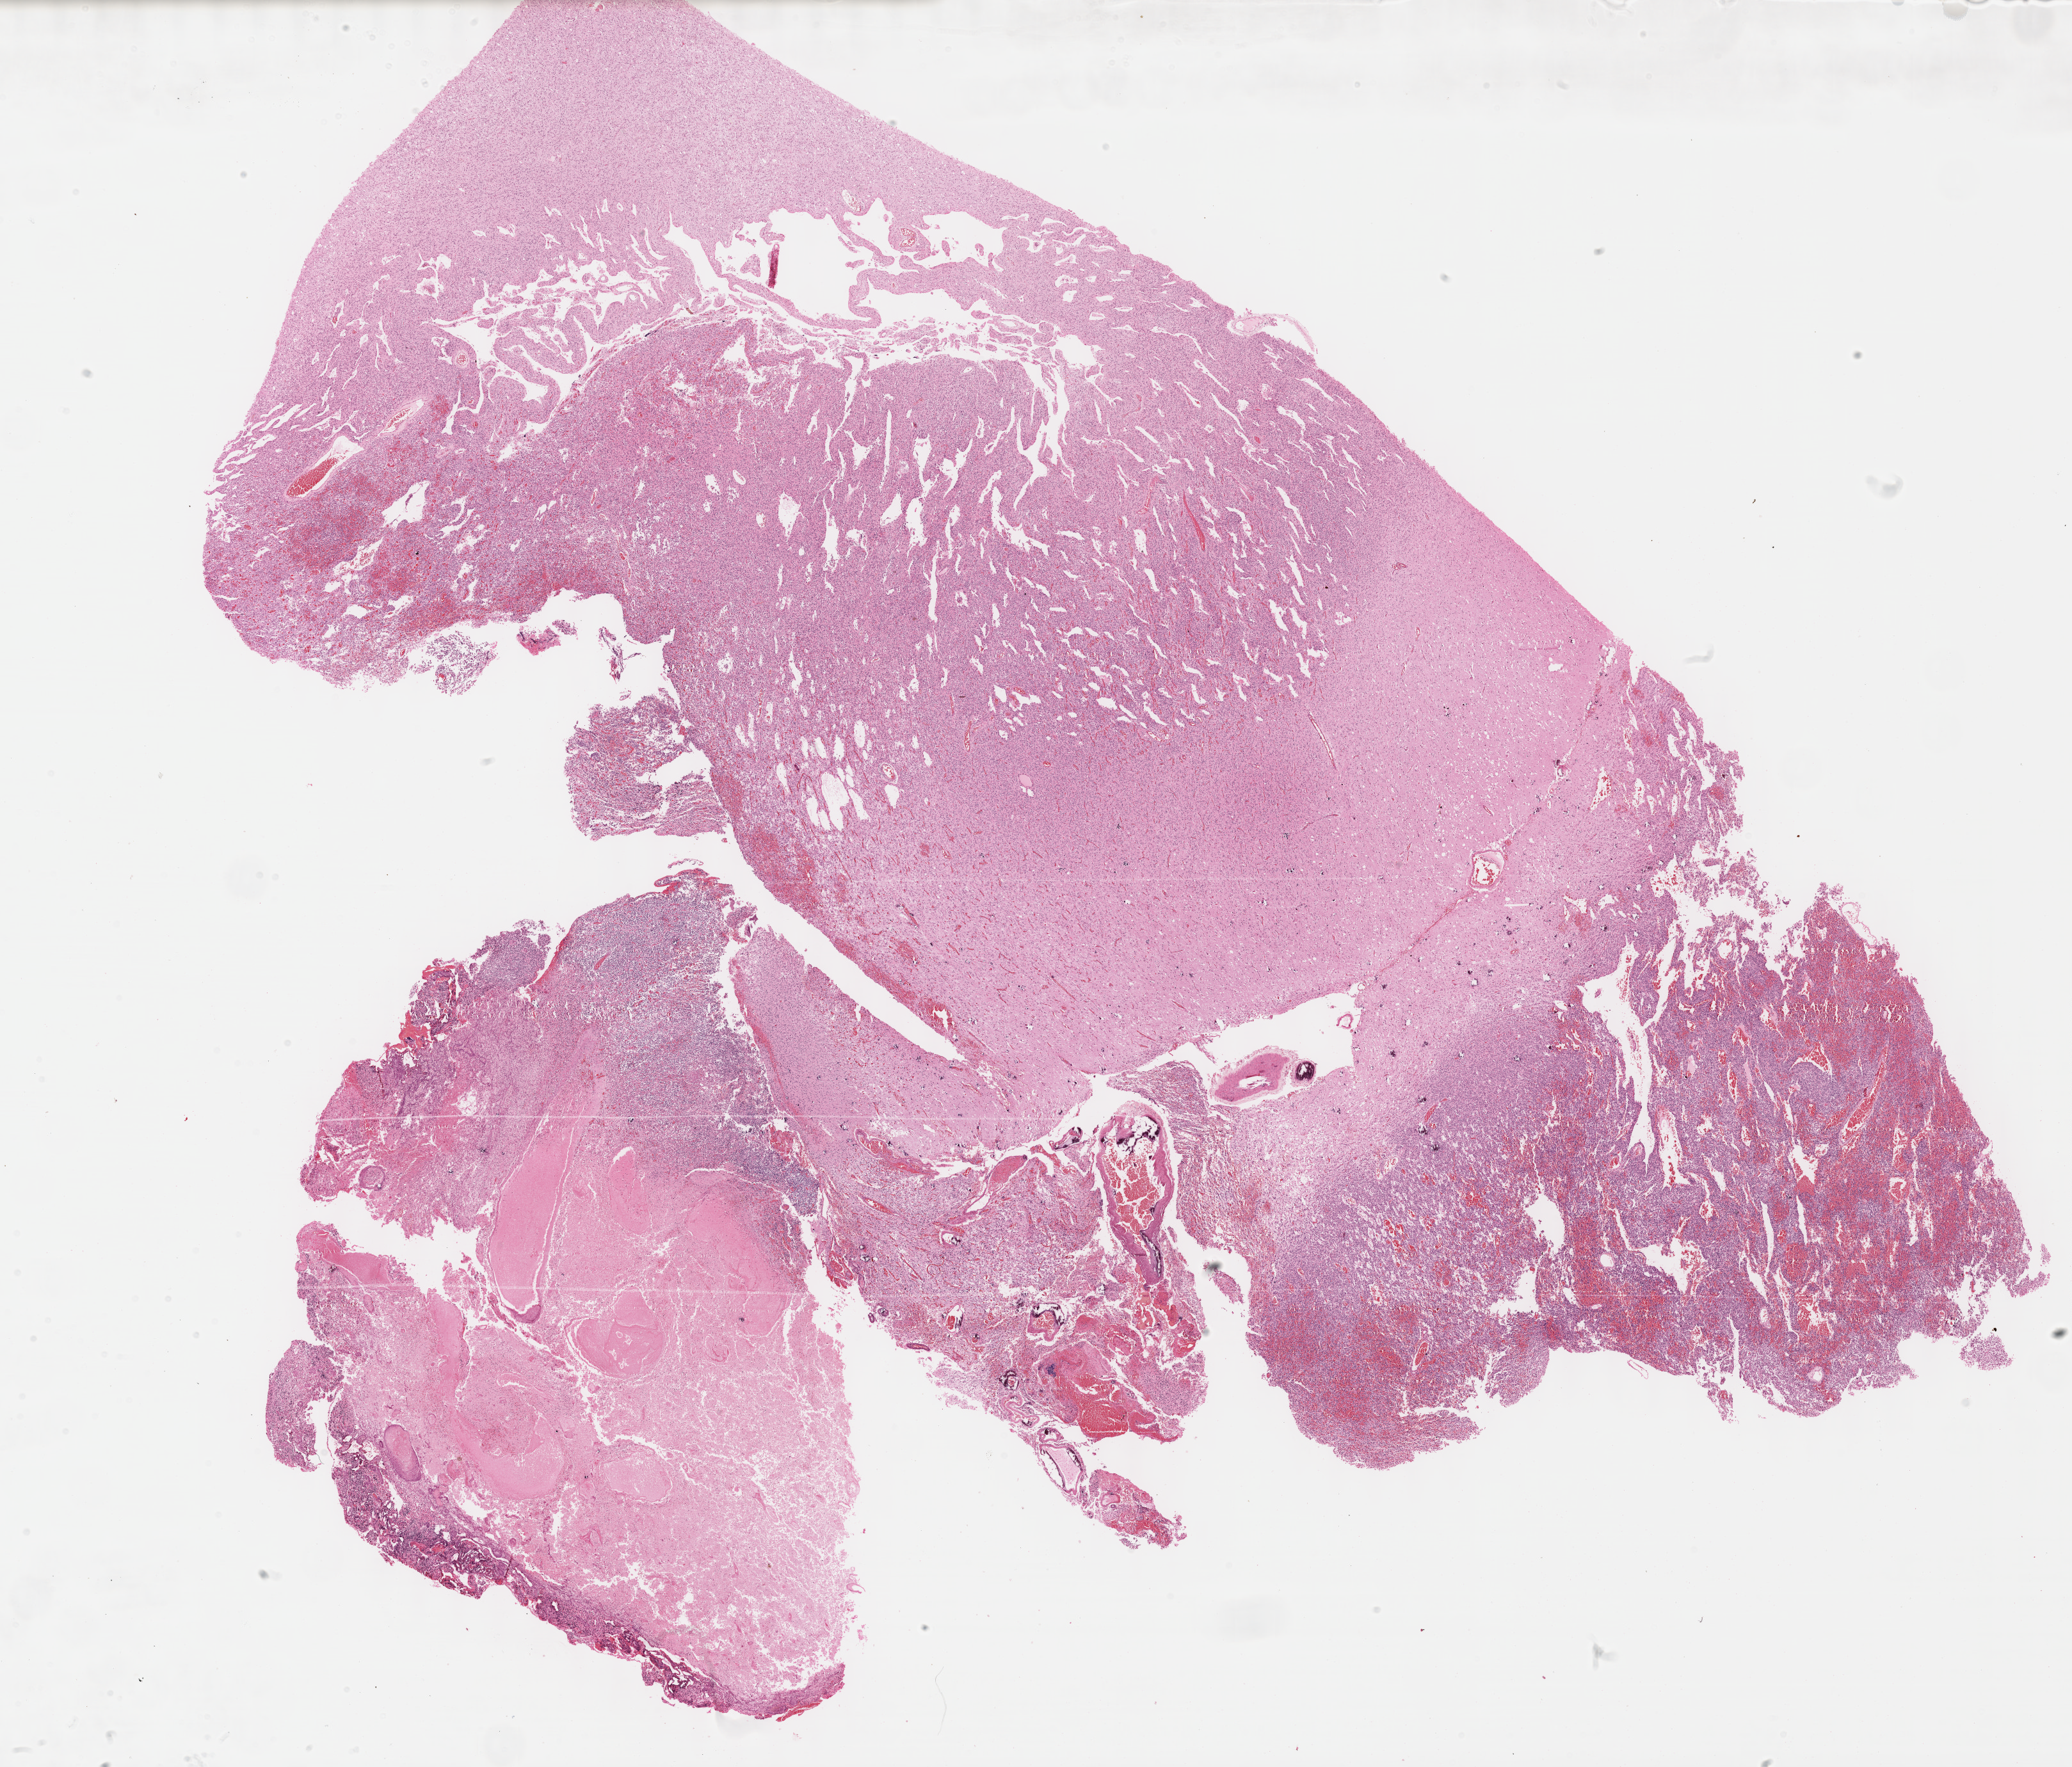
Whole-slide histology image, H&E-stained, low-resolution overview of the scanned area, about 26.2 x 22.3 mm (acquisition: 40x scan). FFPE section. Brain, primary tumour sample. Patient: female, age at initial diagnosis 27 years. Histologic grade: G3 (poorly differentiated).
Laterality: right. Histologic diagnosis: Oligodendroglioma, anaplastic (cerebrum).